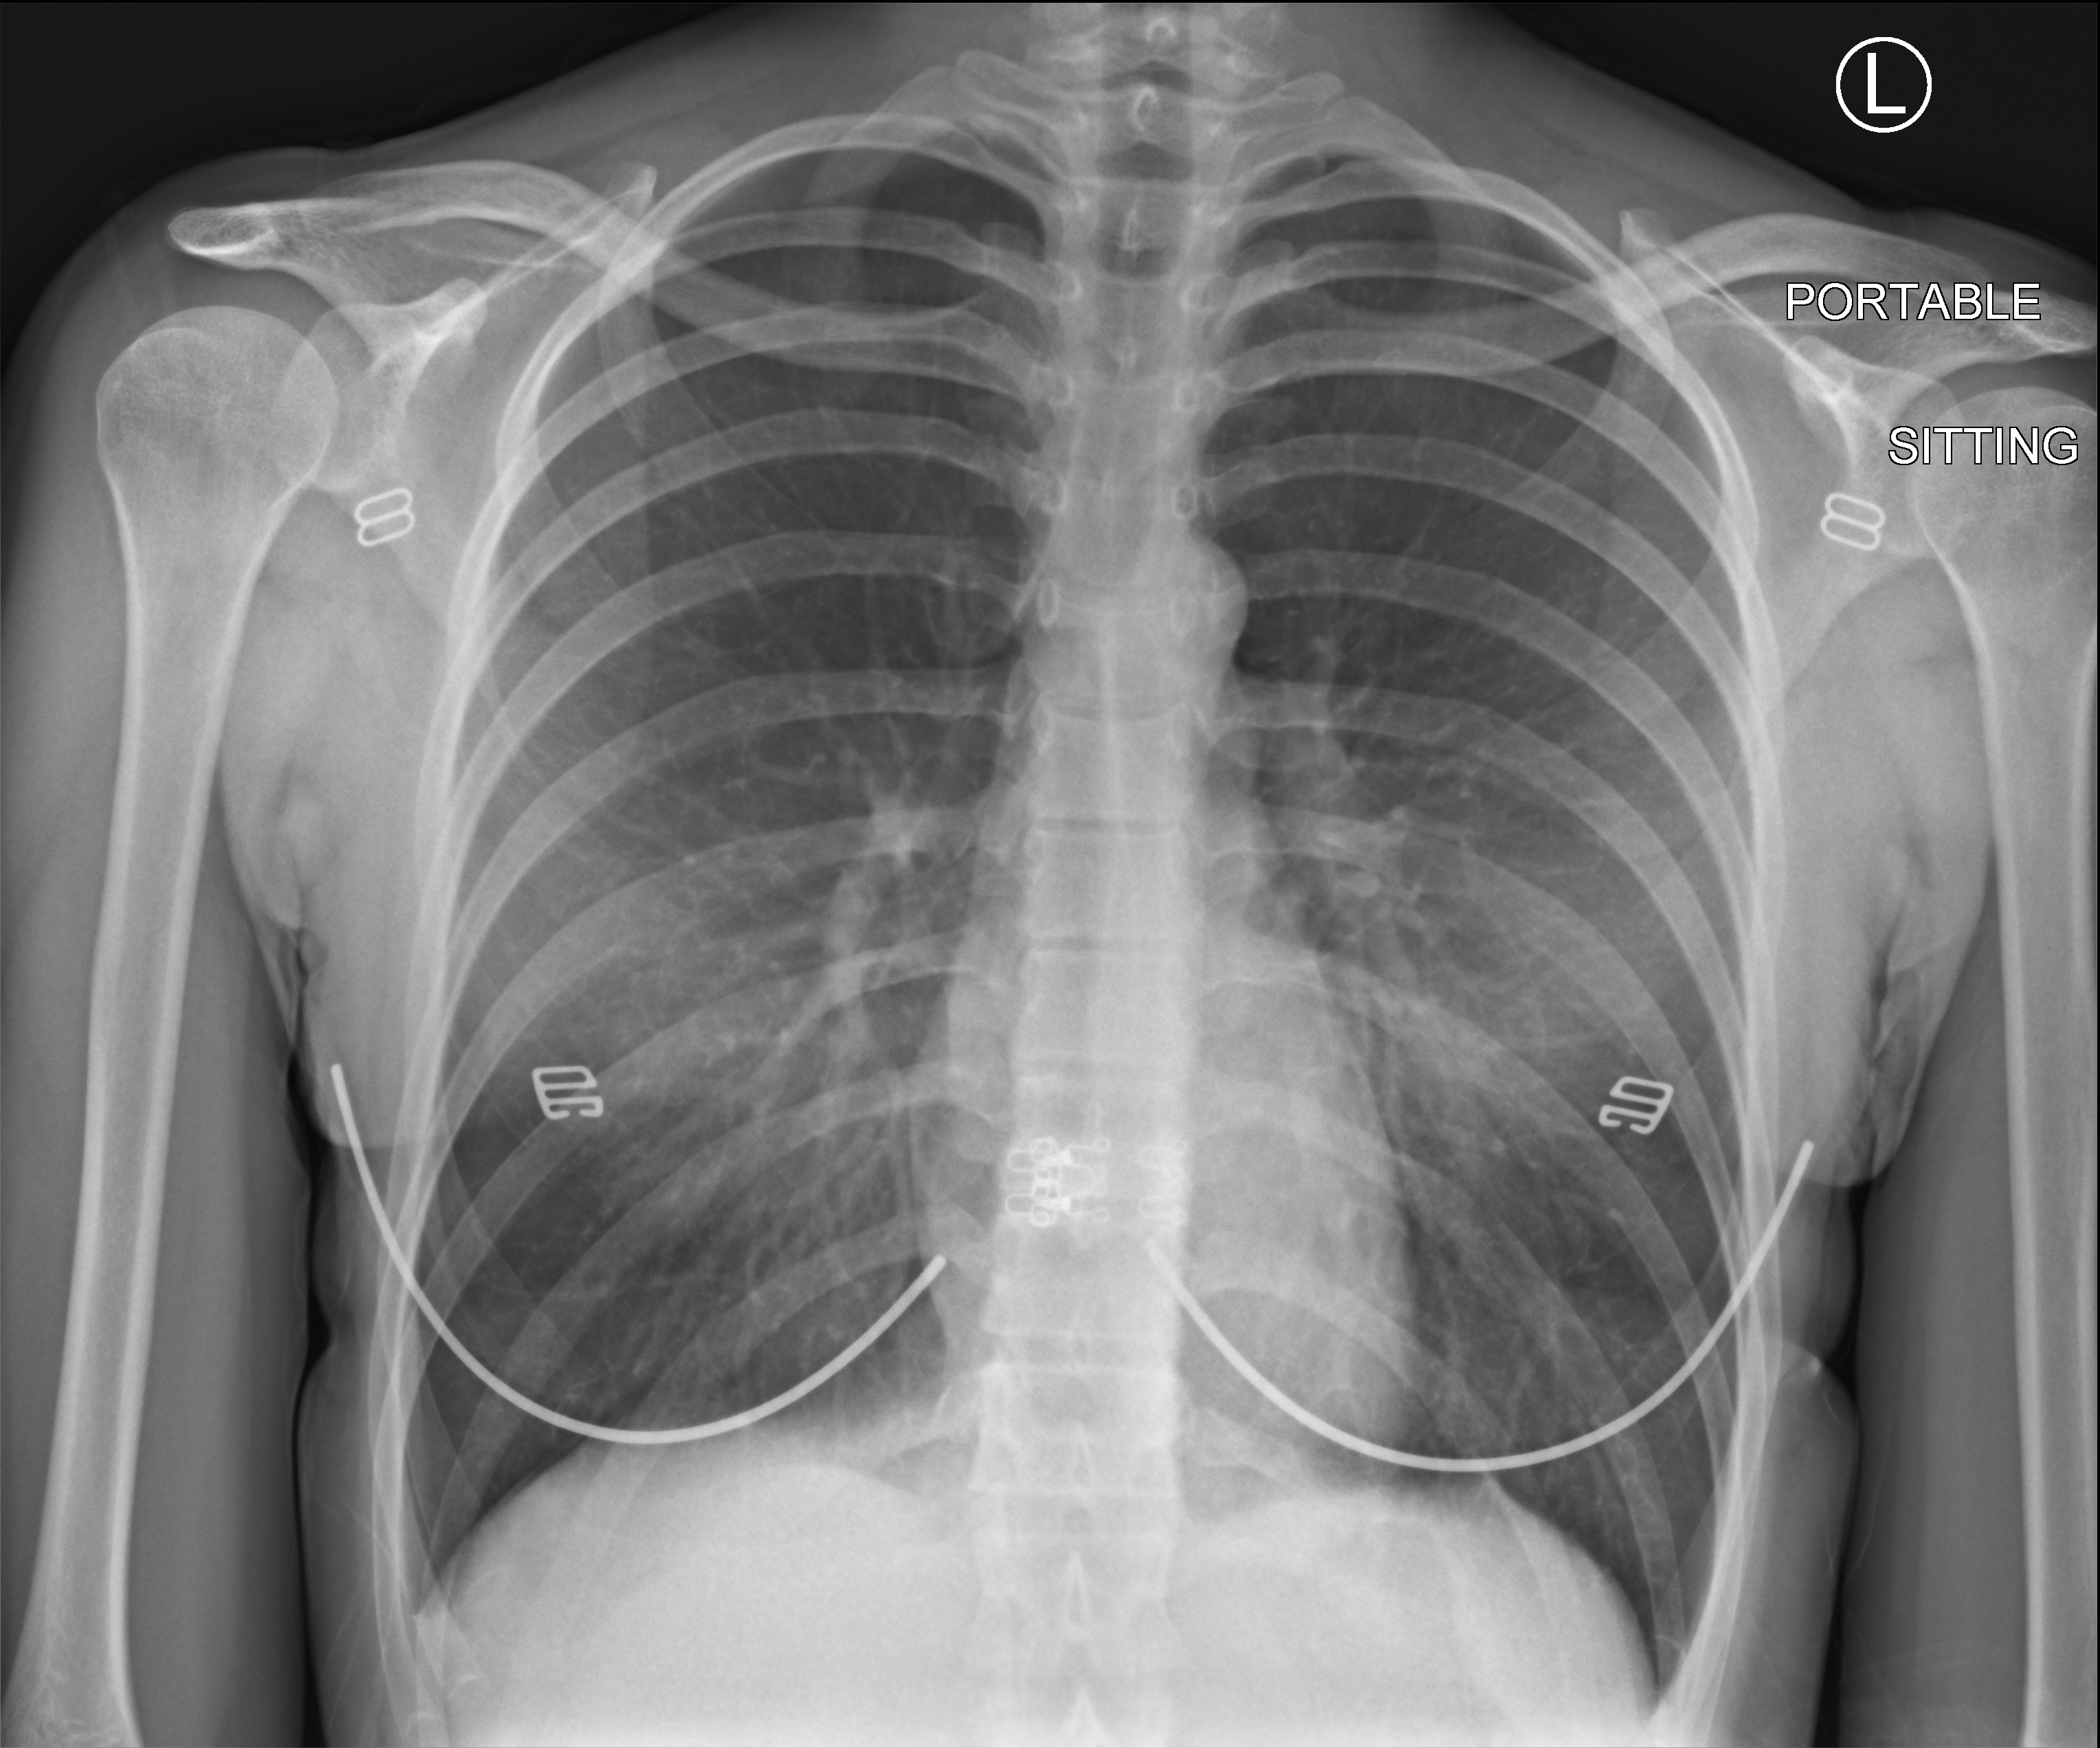
Bedside chest radiograph (computed radiography). Patient hospitalised with COVID-19; female, aged 18–59 years.
From the hospital-stay record, not from the radiograph (when in the stay this image was taken is not recorded): length of hospital stay: 1 day; mechanically ventilated during this hospital stay: no; admitted to intensive care during this hospital stay: no.